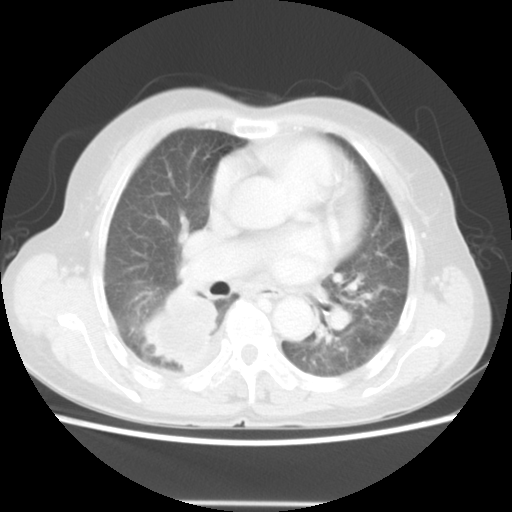
Chest CT, one axial slice. Slice 28 of 52 in the series (ordered by position). Reconstruction kernel STANDARD. Lung window (W 1500 / L -600 HU). 512 × 512 image matrix, field of view 337 × 337 mm. Female patient, age 67 years. Case-level facts recorded for this patient, not image findings: clinical TNM (as recorded): T3 N1 M1.
Structures marked on this image (bounding box drawn by a radiologist):
- lung tumour (recorded histology: adenocarcinoma): box from (x=135, y=285) to (x=223, y=371) px